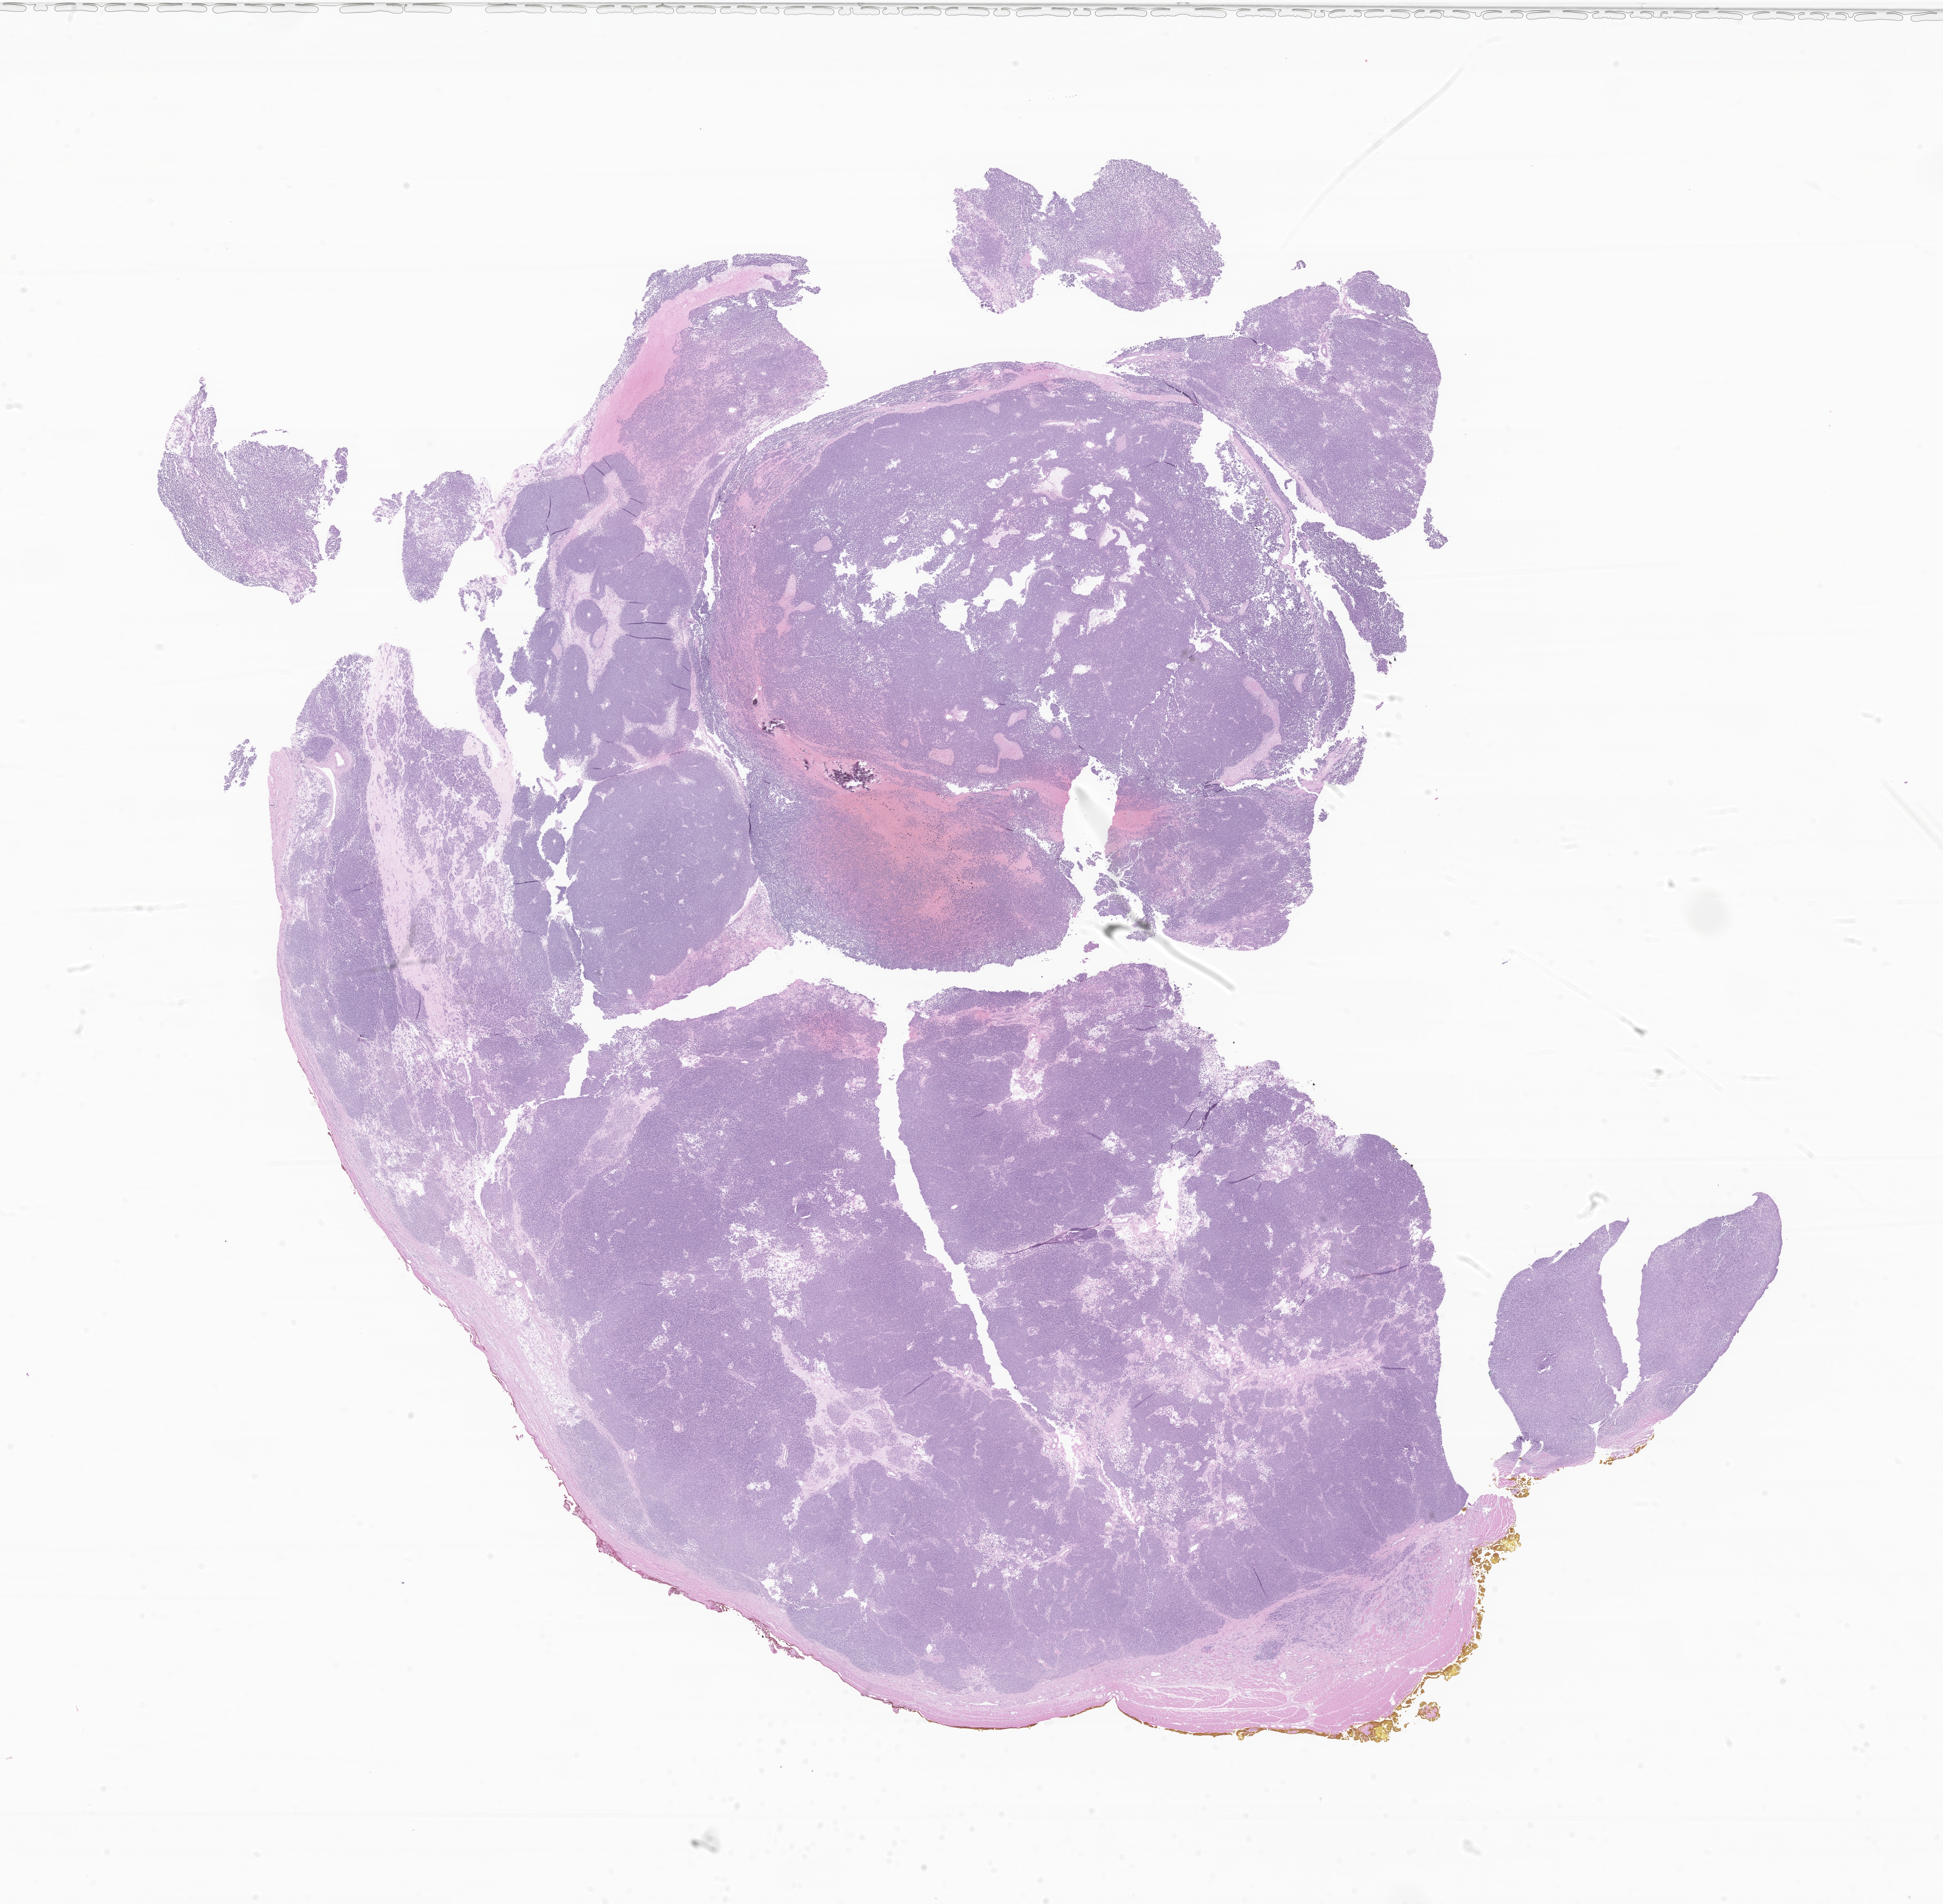
Digitized hematoxylin and eosin (H&E)-stained section of tumor tissue from the head and neck lymph node, whole scanned area (about 22.6 x 22.2 mm) shown as a low-resolution overview. Formalin-fixed paraffin-embedded section. Female patient, age 33 months (2 years 9 months).
• recorded diagnosis: Sarcoma, NOS